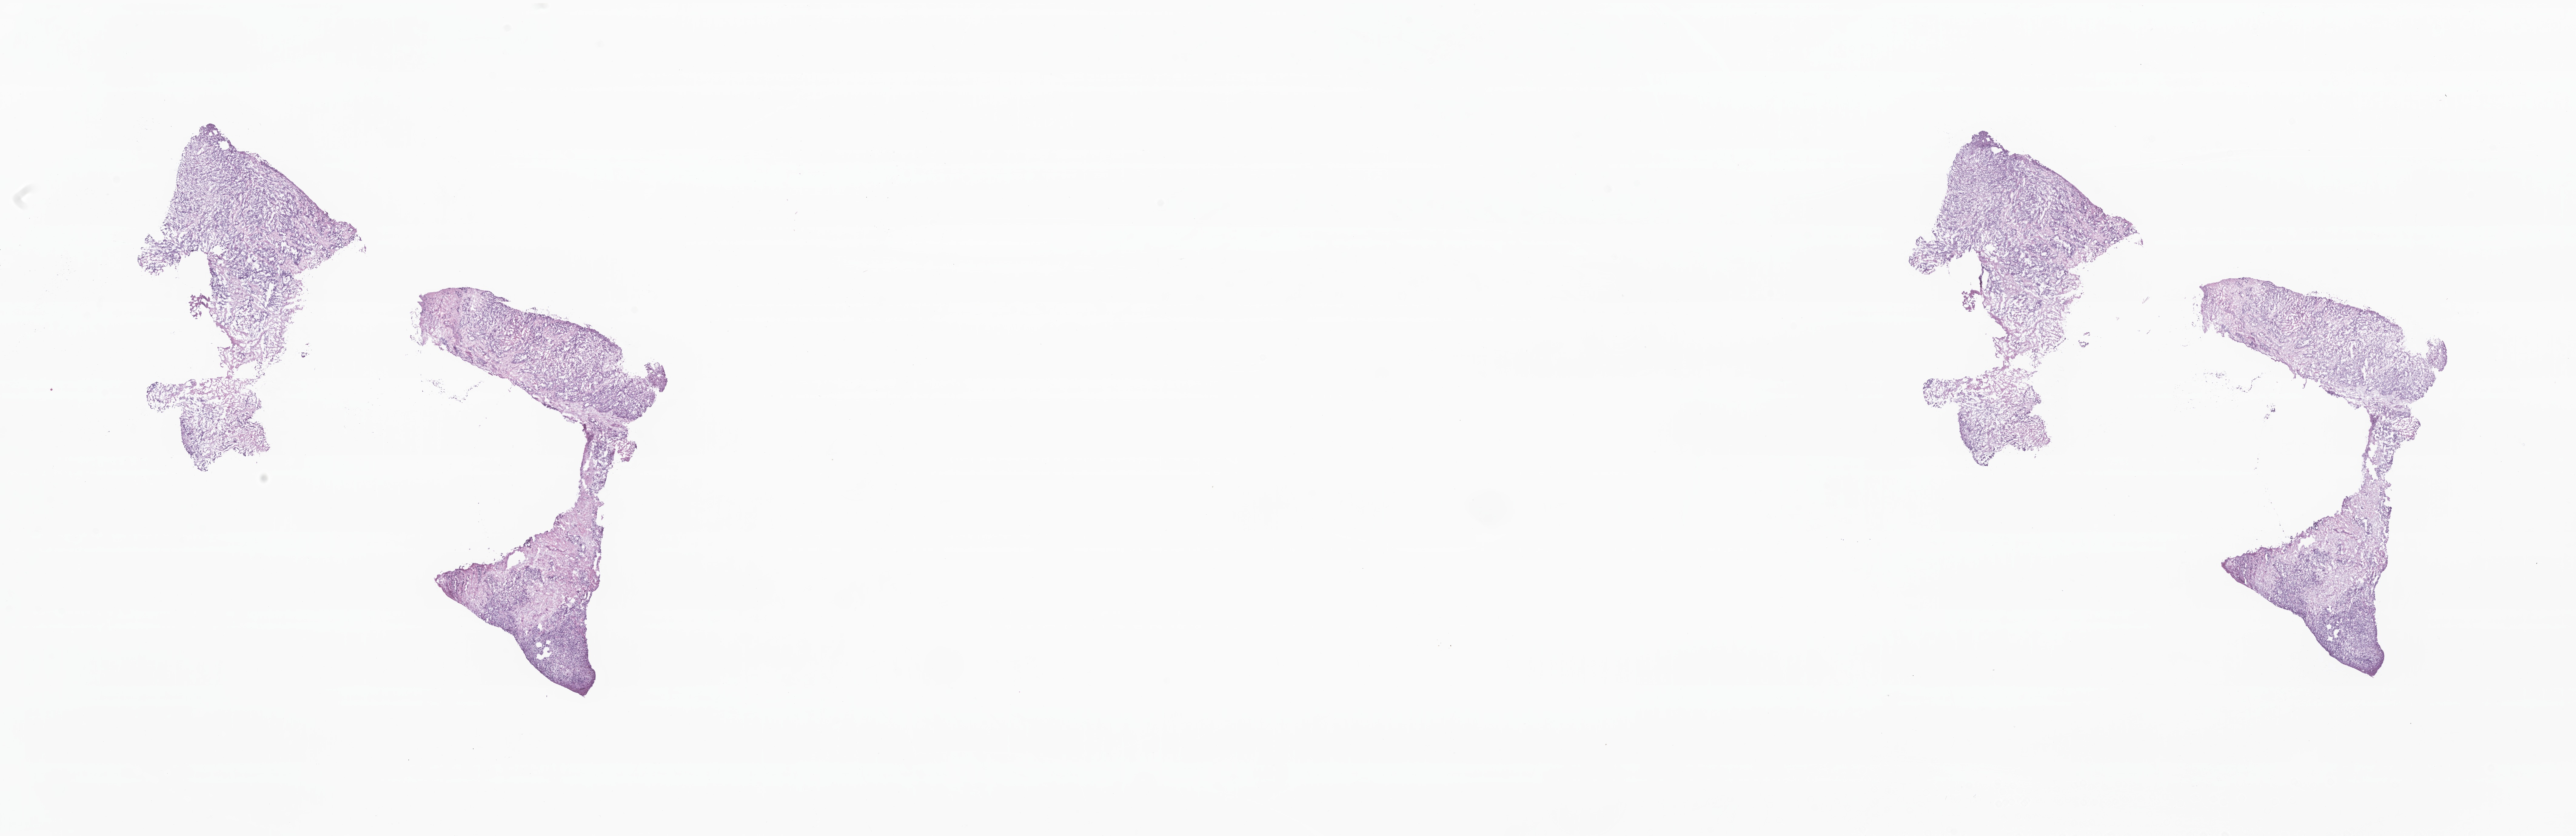
Whole-slide image, haematoxylin and eosin stain, whole scanned area (about 35.8 x 11.6 mm) shown as a low-resolution overview. Frozen section (tissue freezing medium). Metastatic tumor tissue, resected from liver. Male patient; age at initial diagnosis 65 years. Pathologist review of this section (percent, as recorded): tumor cells 85%, tumor nuclei 85%, stromal cells 14%, necrosis 1%, normal cells 0%. Inflammatory infiltration, as recorded: lymphocyte infiltration 3%, monocyte infiltration 2%, neutrophil infiltration 5%.
Patient diagnosis (primary): Adenocarcinoma, NOS. Section: top of the tissue portion.